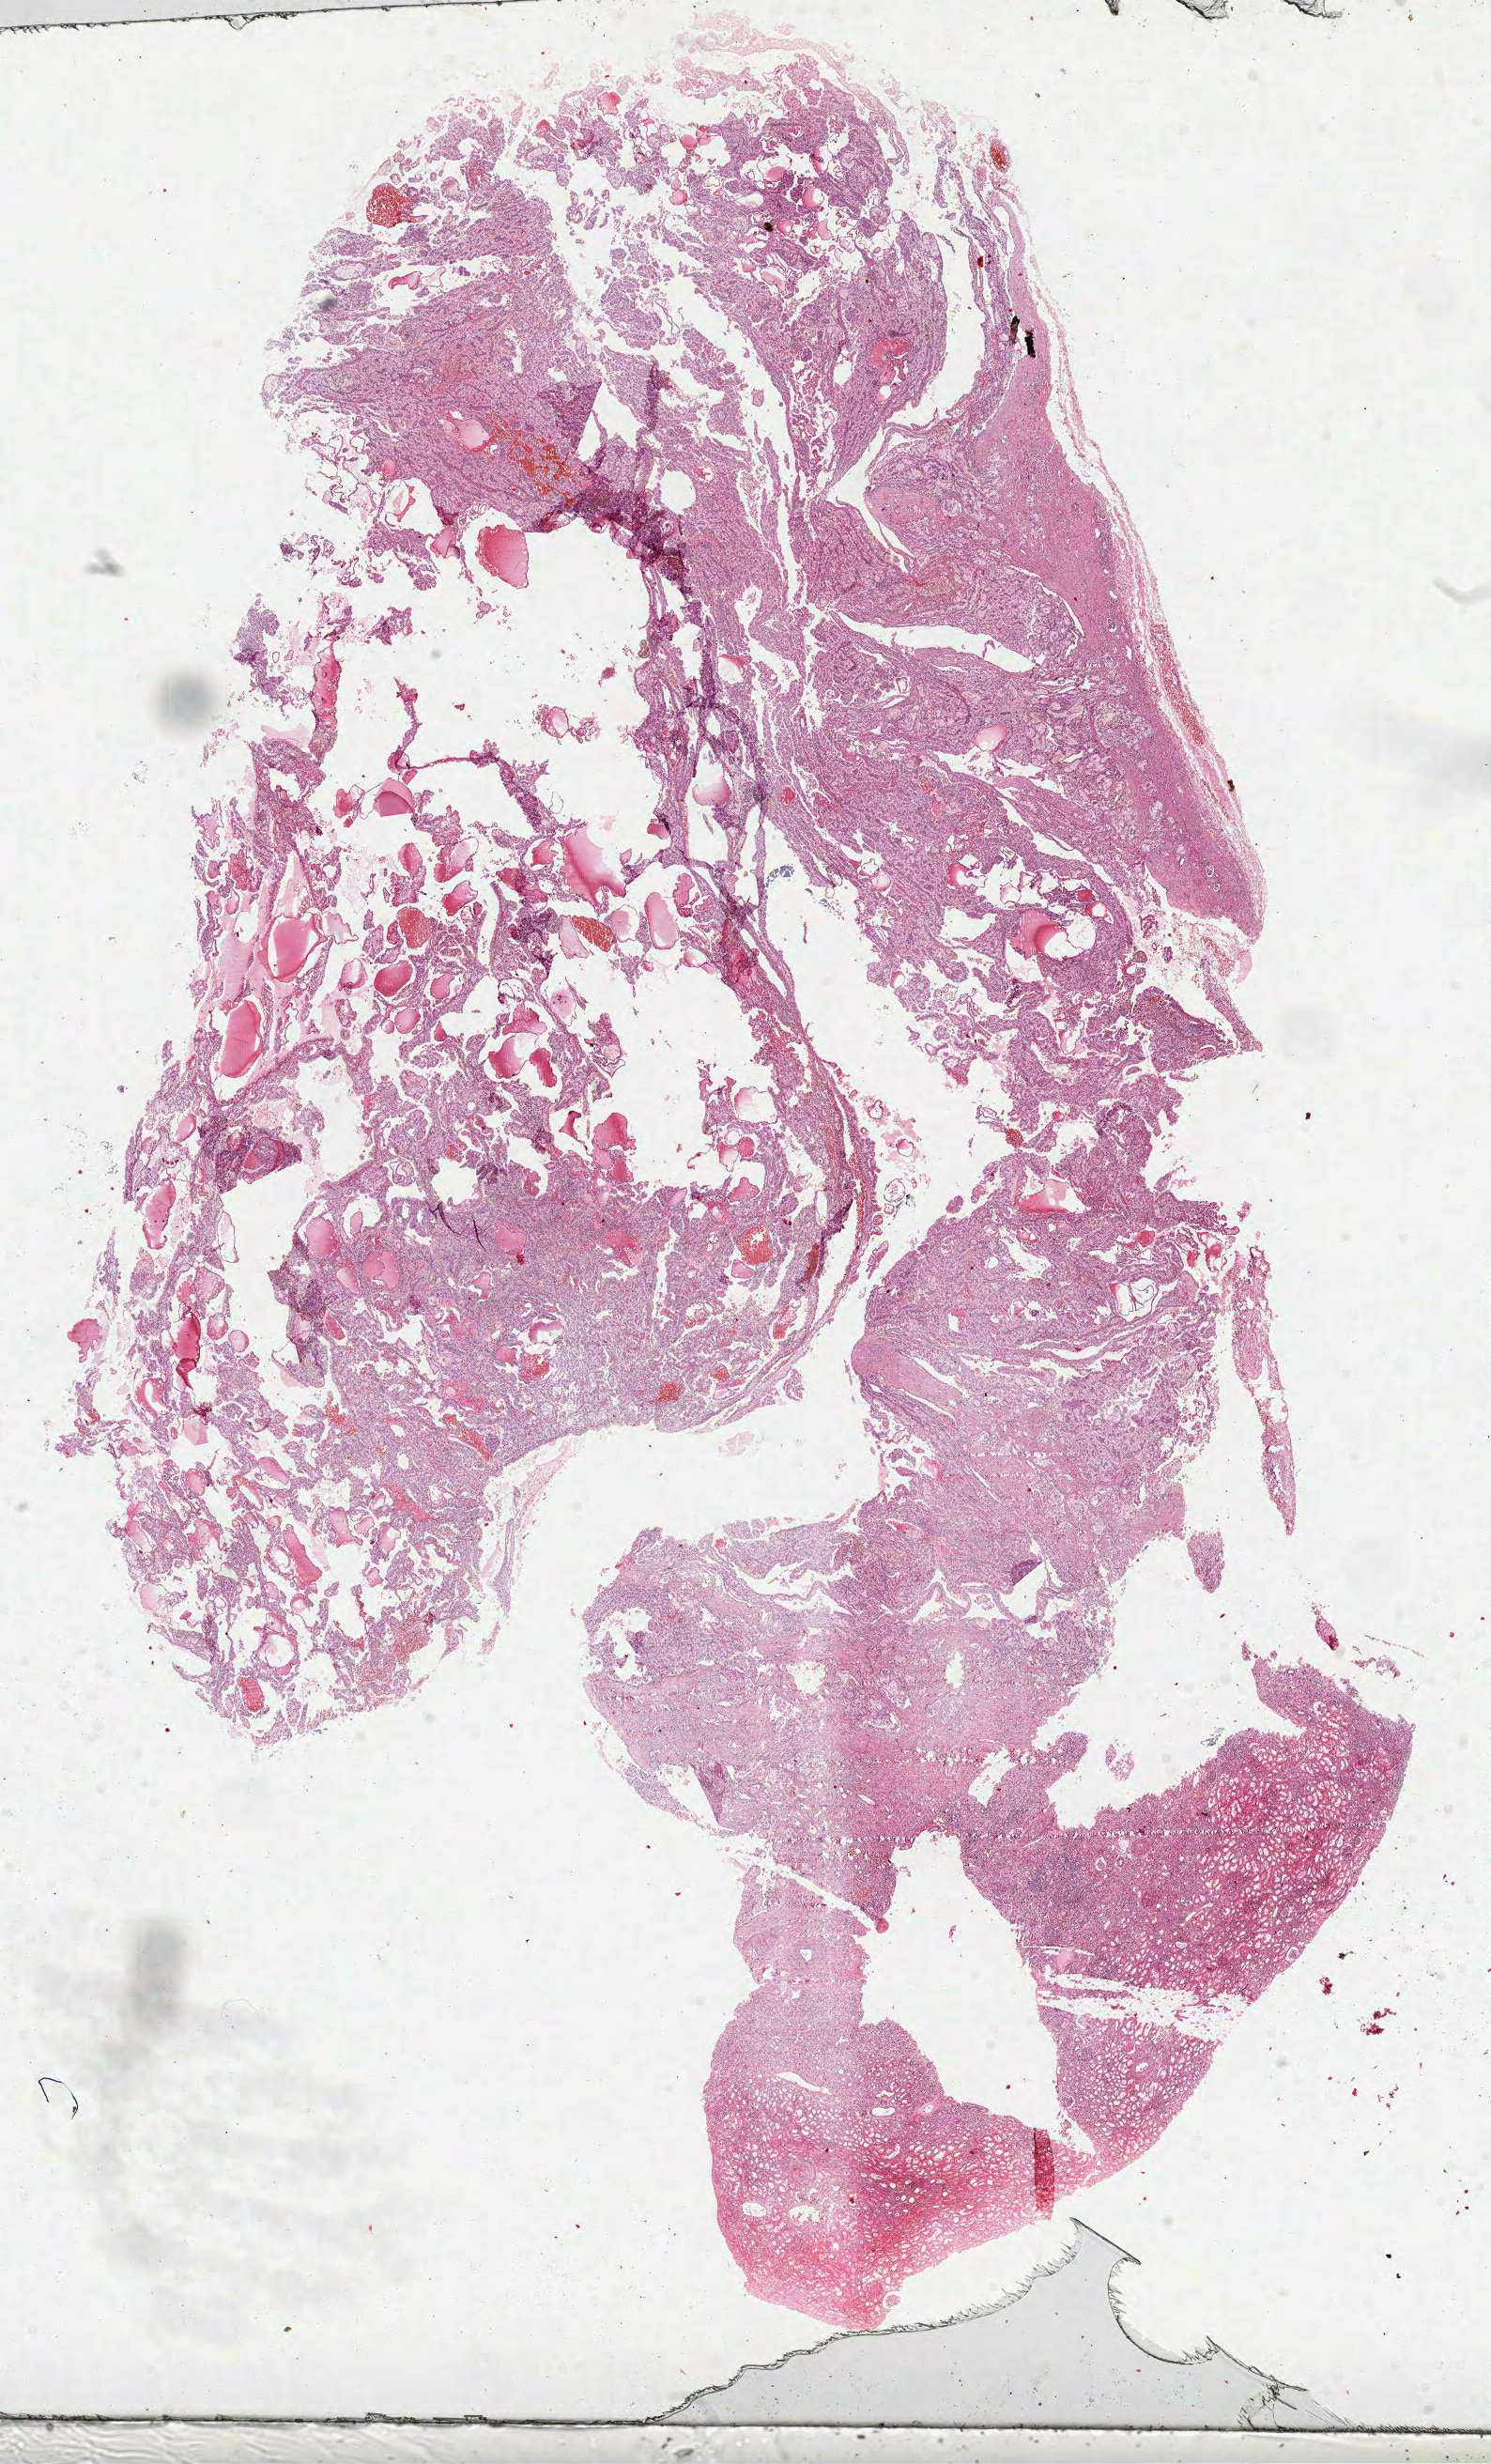
Digitized Hematoxylin and eosin (H&E) stained tissue section (whole slide) — whole scanned area (about 12.8 x 21.2 mm, from a 40x scan) shown as a low-resolution overview, formalin-fixed paraffin-embedded (FFPE) diagnostic section, primary tumour sample from the kidney. Male, age 42 years at initial diagnosis.
Pathologic diagnosis: Papillary adenocarcinoma, NOS. AJCC pathologic stage: I (6th edition).